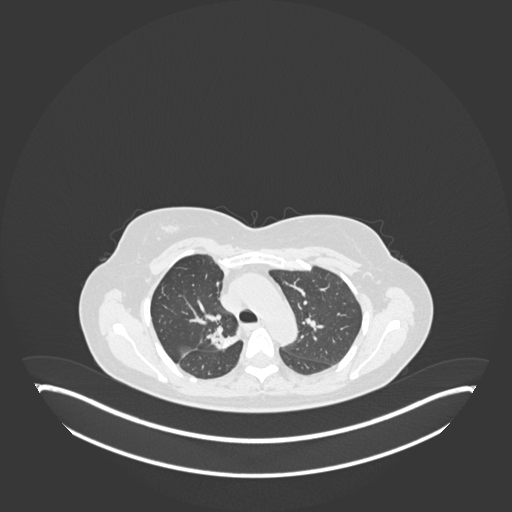
Chest CT, one axial slice. Position 124 of 181 along the scan axis. Lung window (W 1500 / L -600 HU). 1 mm slice thickness. 512 × 512 image matrix, field of view 500 × 500 mm. Female patient, age 65 years. Case-level facts recorded for this patient, not image findings: clinical TNM (as recorded): T1b N0 M0; histopathological grade: G2.
Annotated regions visible in this slice (bounding box drawn by a radiologist):
- lung tumour (recorded histology: adenocarcinoma): bounding box [x1, y1, x2, y2] px = [202, 326, 241, 355]